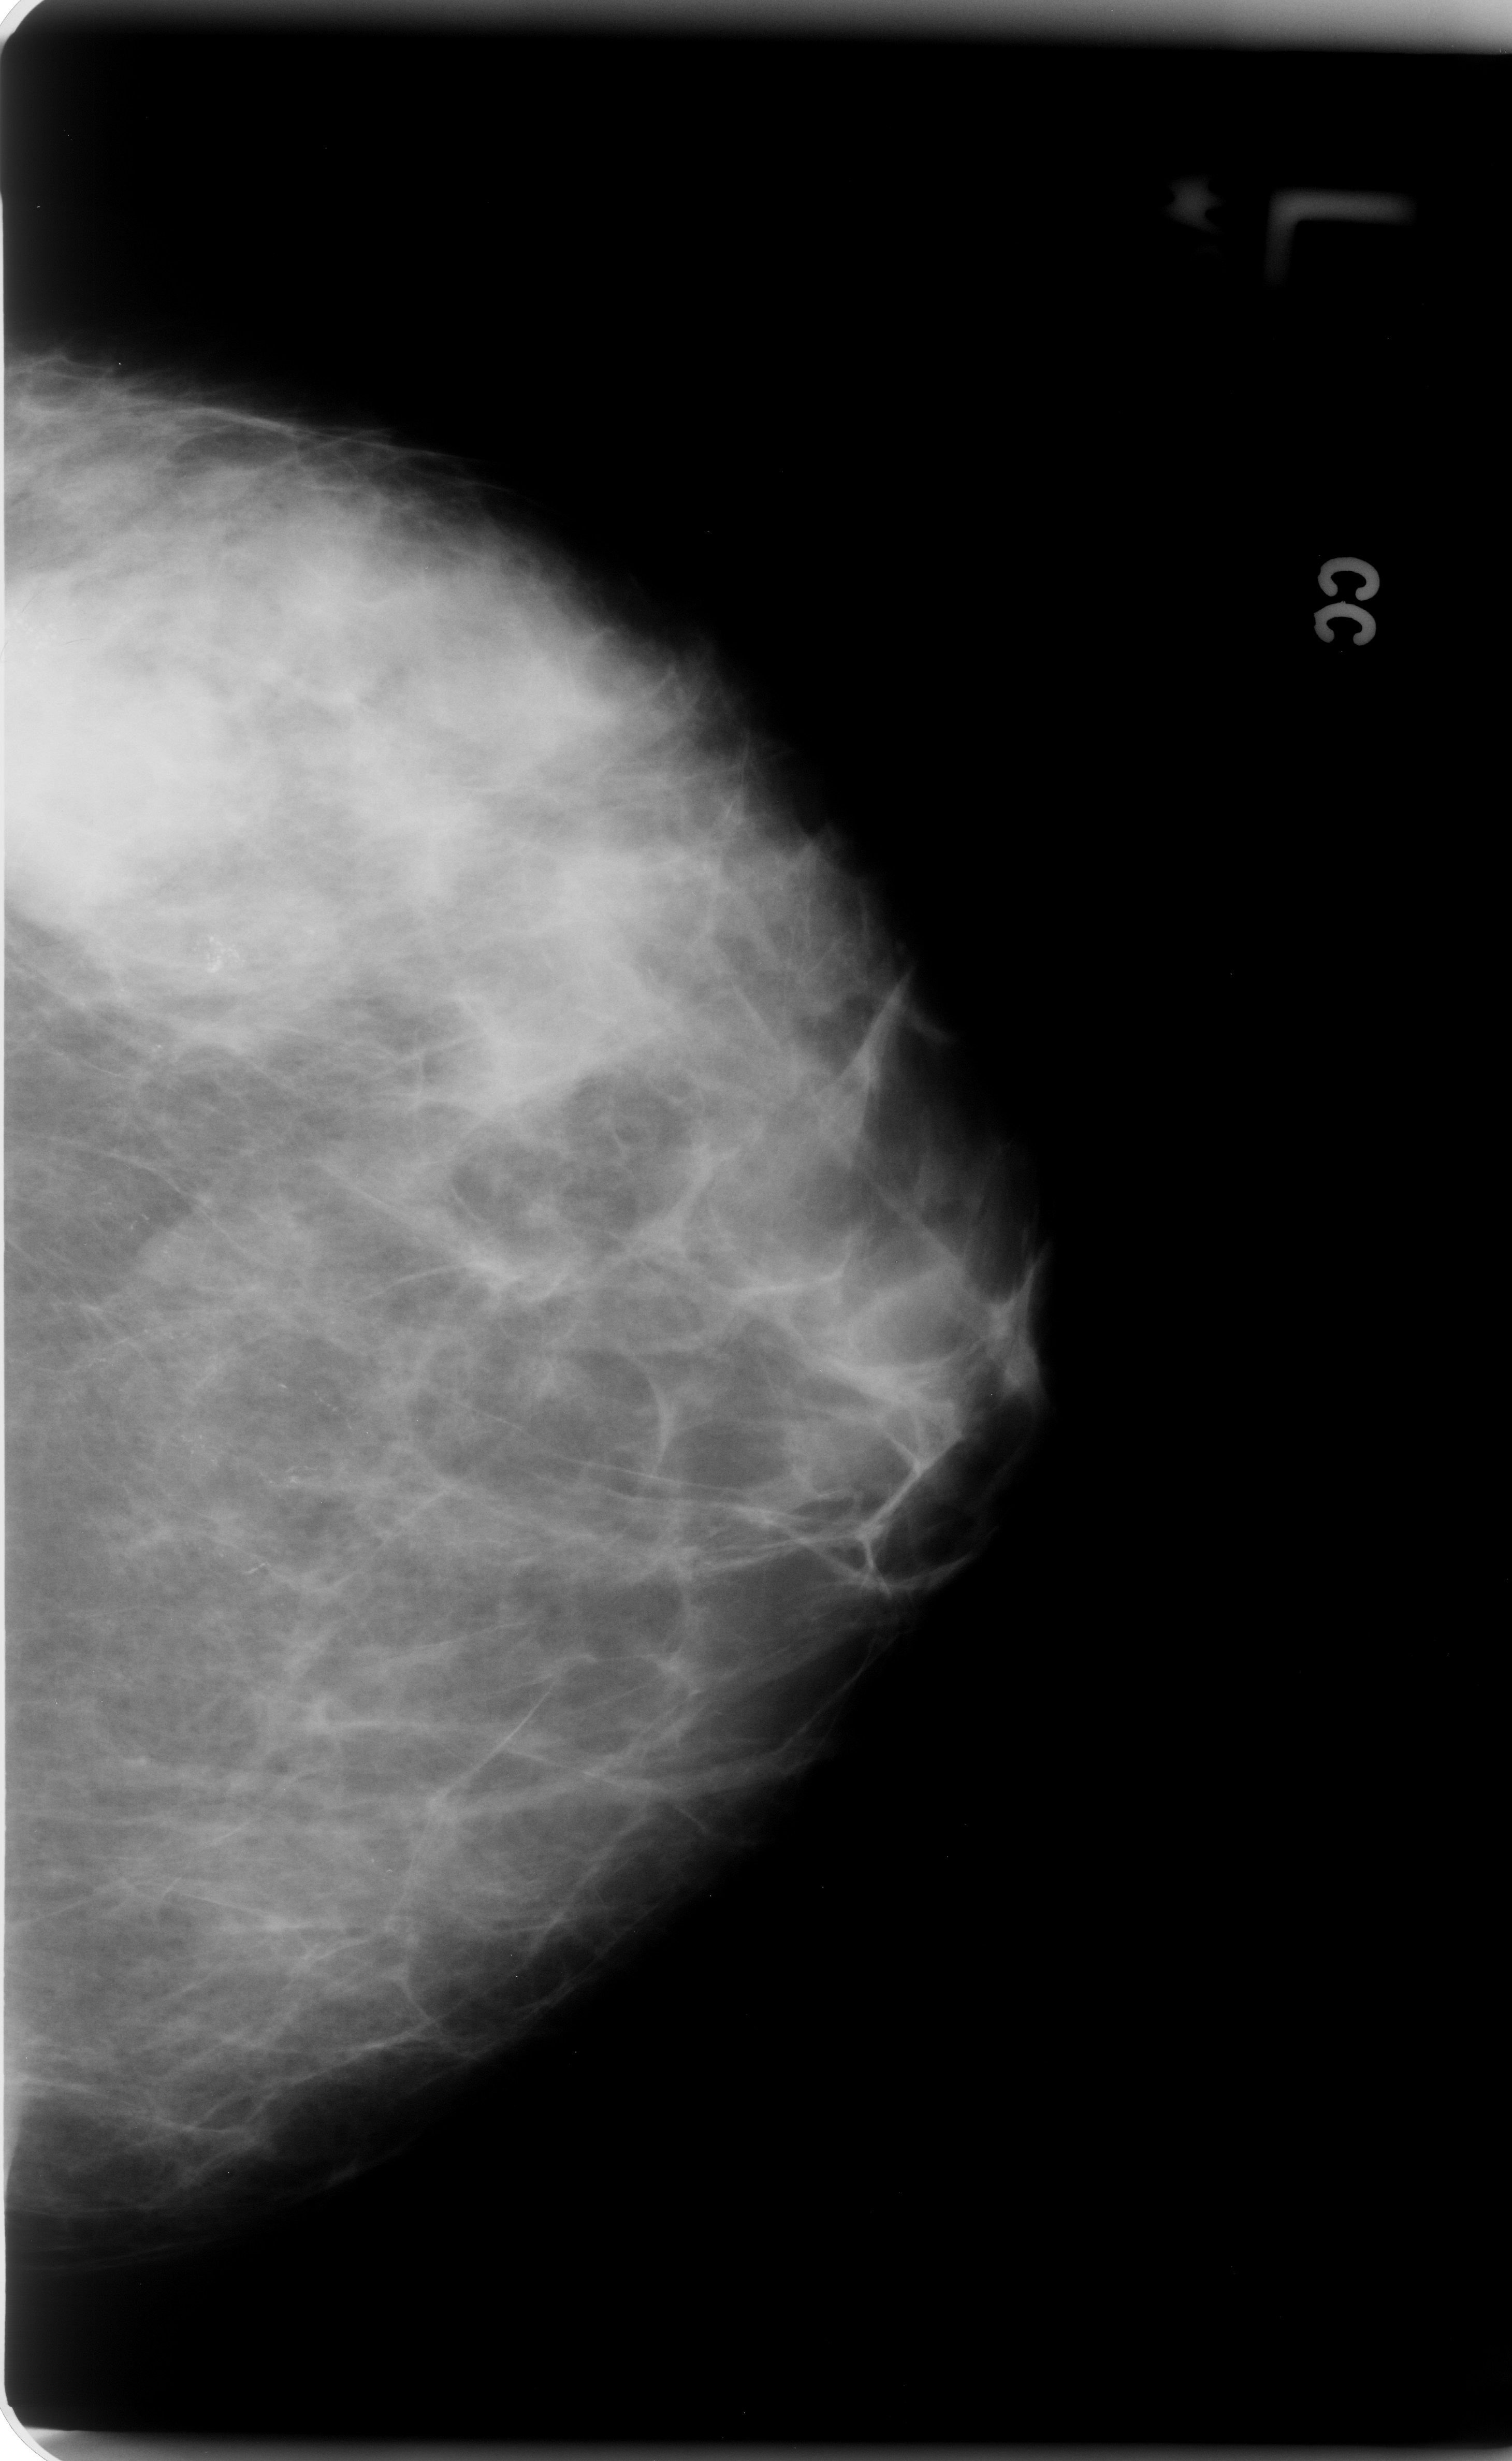
Scanned film-screen mammogram; left breast; craniocaudal (CC) view; breast composition: scattered fibroglandular densities (BI-RADS density category 2 of 4); 1512 × 2461 image matrix.
Marked abnormalities (boxes around the expert regions of interest):
- Finding 1 of 2: calcifications, morphology pleomorphic / fine linear branching, distribution regional; BI-RADS assessment category 5; pathology (as recorded): malignant: box from (x=12, y=414) to (x=142, y=581) px
- Finding 2 of 2: calcifications, morphology pleomorphic / fine linear branching, distribution regional; BI-RADS assessment category 5; subtlety rating 3 on a 1 (subtle) to 5 (obvious) scale; pathology (as recorded): malignant: (x=173, y=903)–(x=295, y=1012)